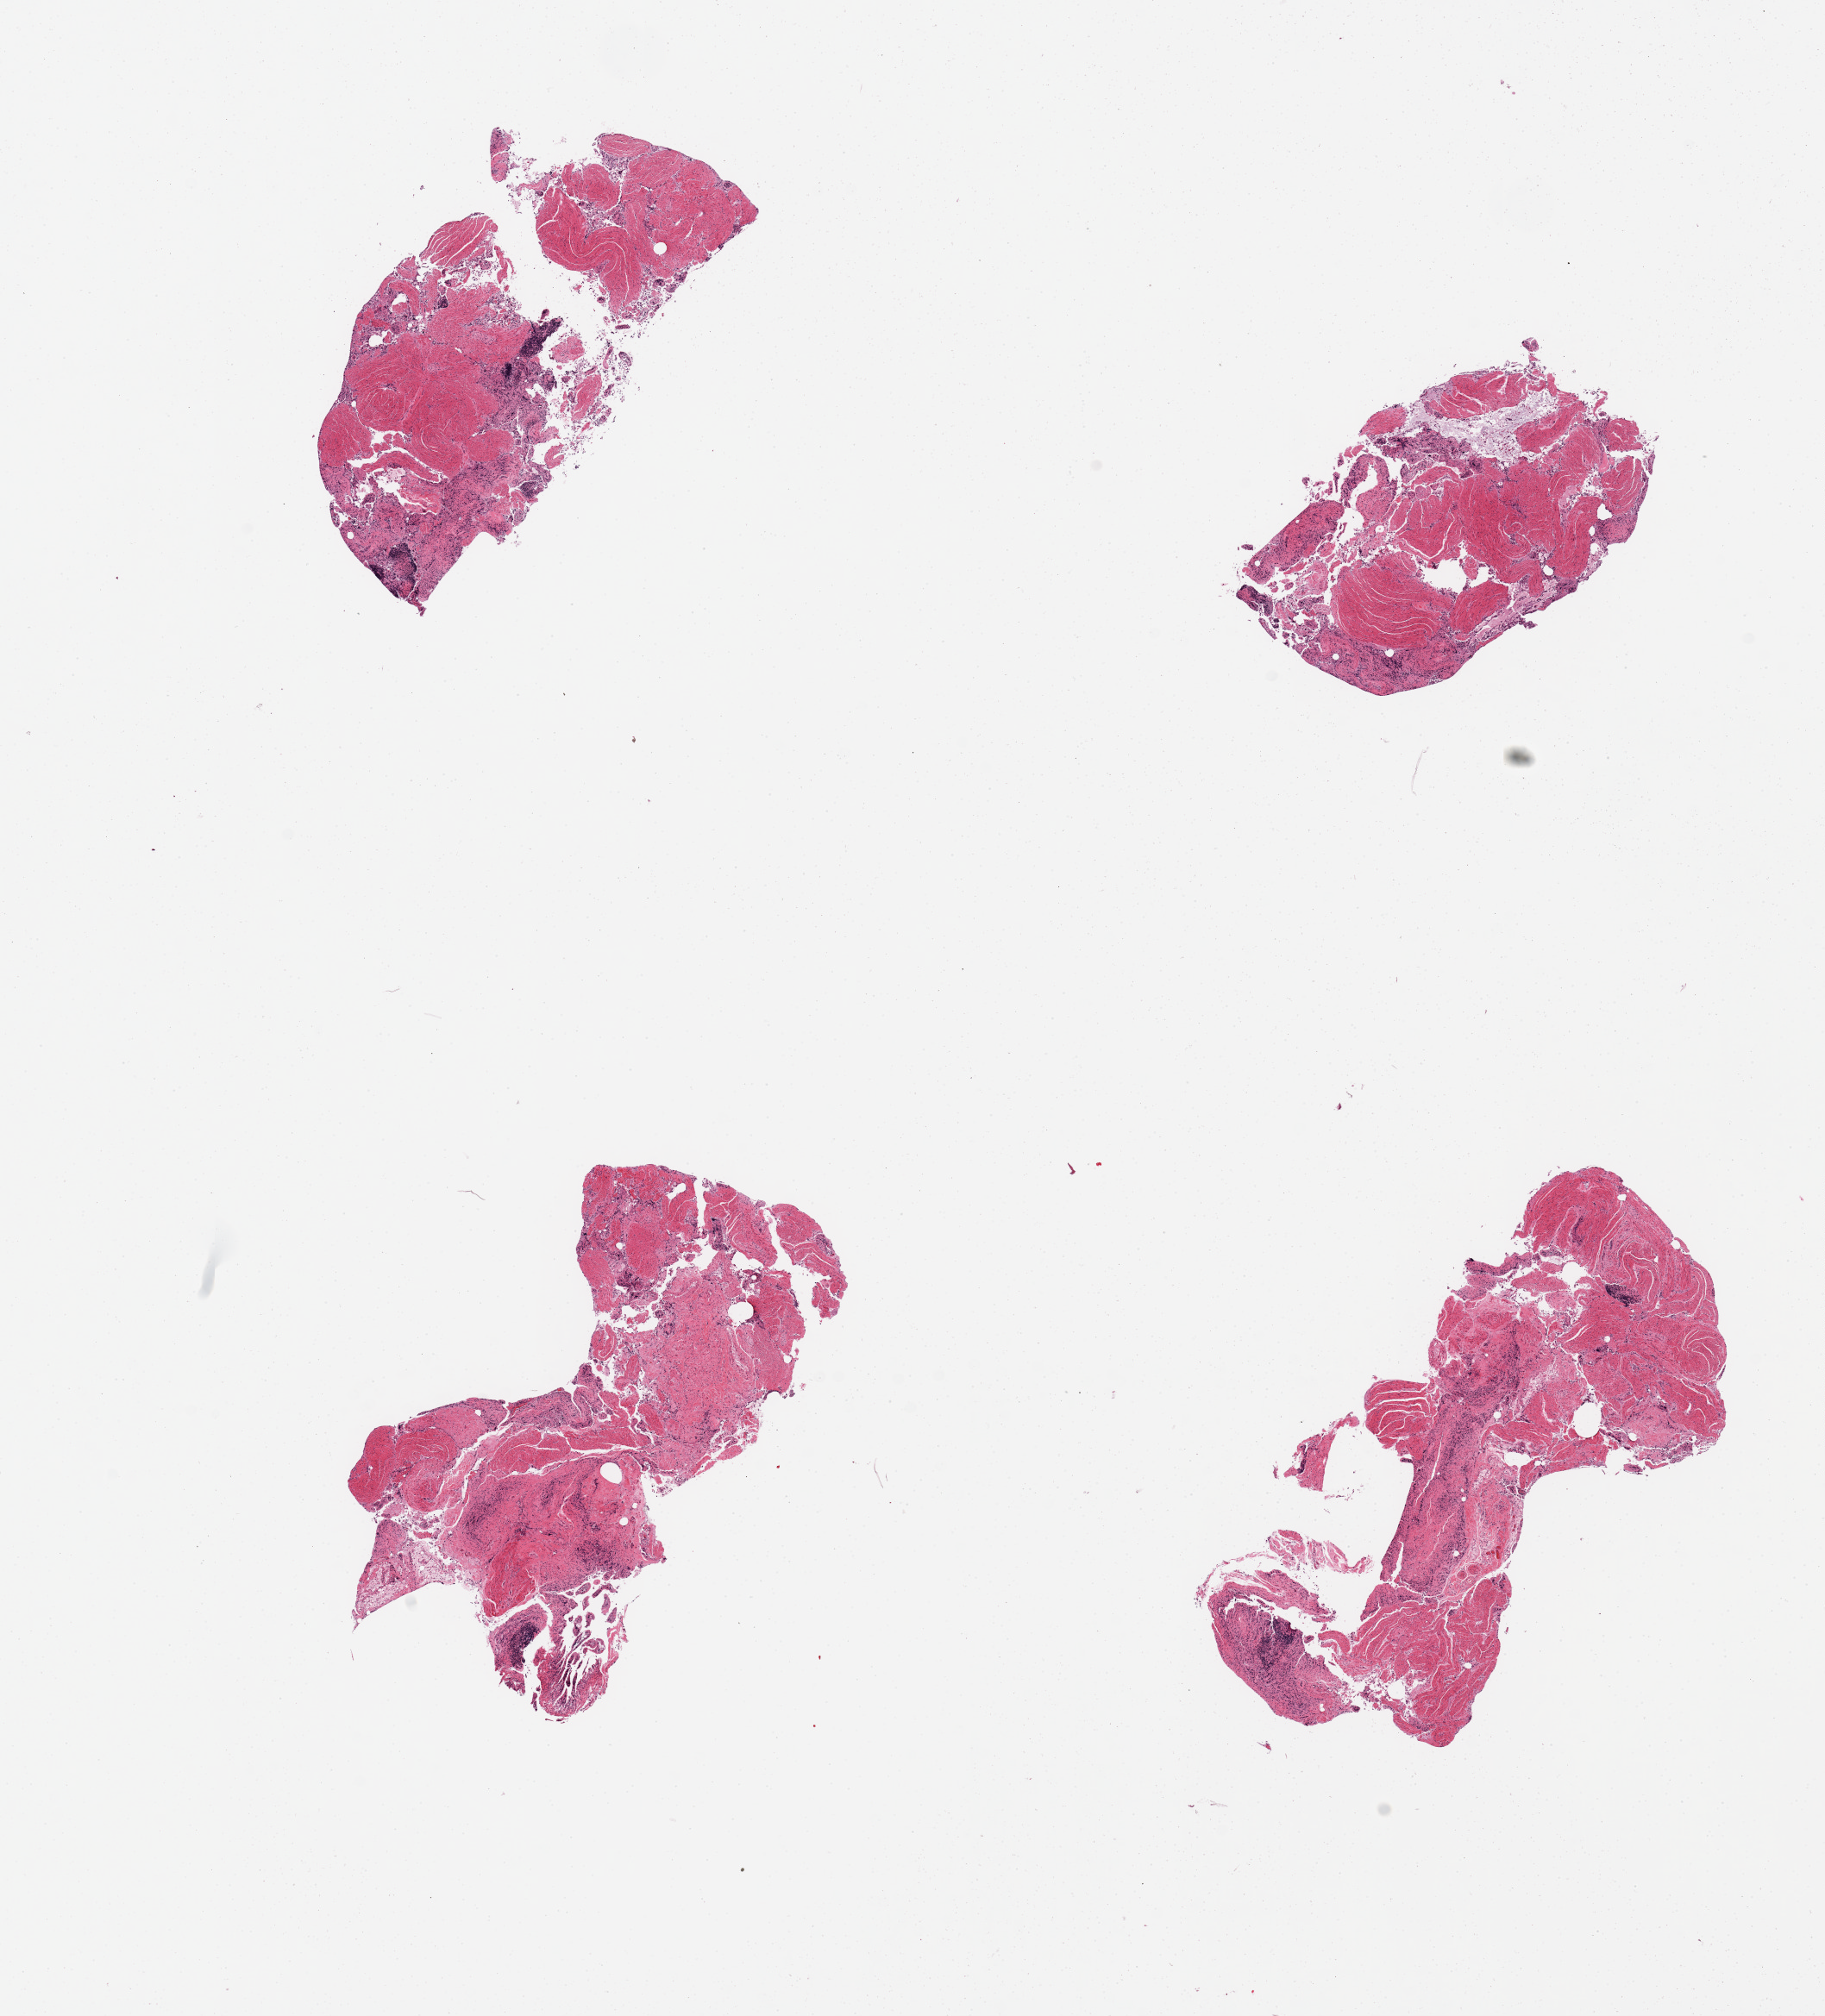
Whole-slide image, hematoxylin and eosin (H&E) stain, brightfield, whole scanned area (about 16.7 x 18.5 mm, from a 20x scan) shown as a low-resolution overview; PAXgene-fixed paraffin-embedded (PFPE) section; target tissue: ileum; tissue donor sample. Male donor.
* pathologist's review note for this sample: 4 pieces, markedly autolyzed, ~10% lymphoid elements